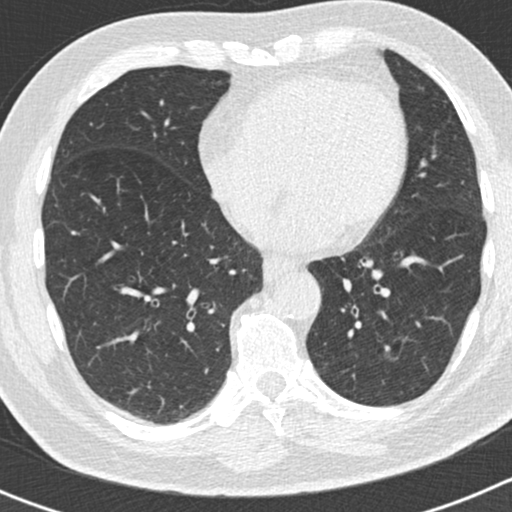
Low-dose screening chest CT, axial slice; second screening round (one year after baseline); lung window (W 1500 / L -600 HU); 2 mm slice thickness; 512 × 512 image matrix. Male, age 66 years at enrolment.
Expert-annotated lung lesion, box from (x=344, y=318) to (x=419, y=401) px. Screening reader's record for this exam (one nodule recorded; not confirmed to be the boxed lesion): non-calcified nodule or mass ≥4 mm, left lower lobe, 50 × 33 mm, smooth margins, pre-existing on the prior screen: yes; interval growth: yes. Lung cancer was diagnosed 440 days after this screen: adenocarcinoma, NOS, left lower lobe, poorly differentiated (G3), stage IB (AJCC 6th edition), 38 mm at pathology.